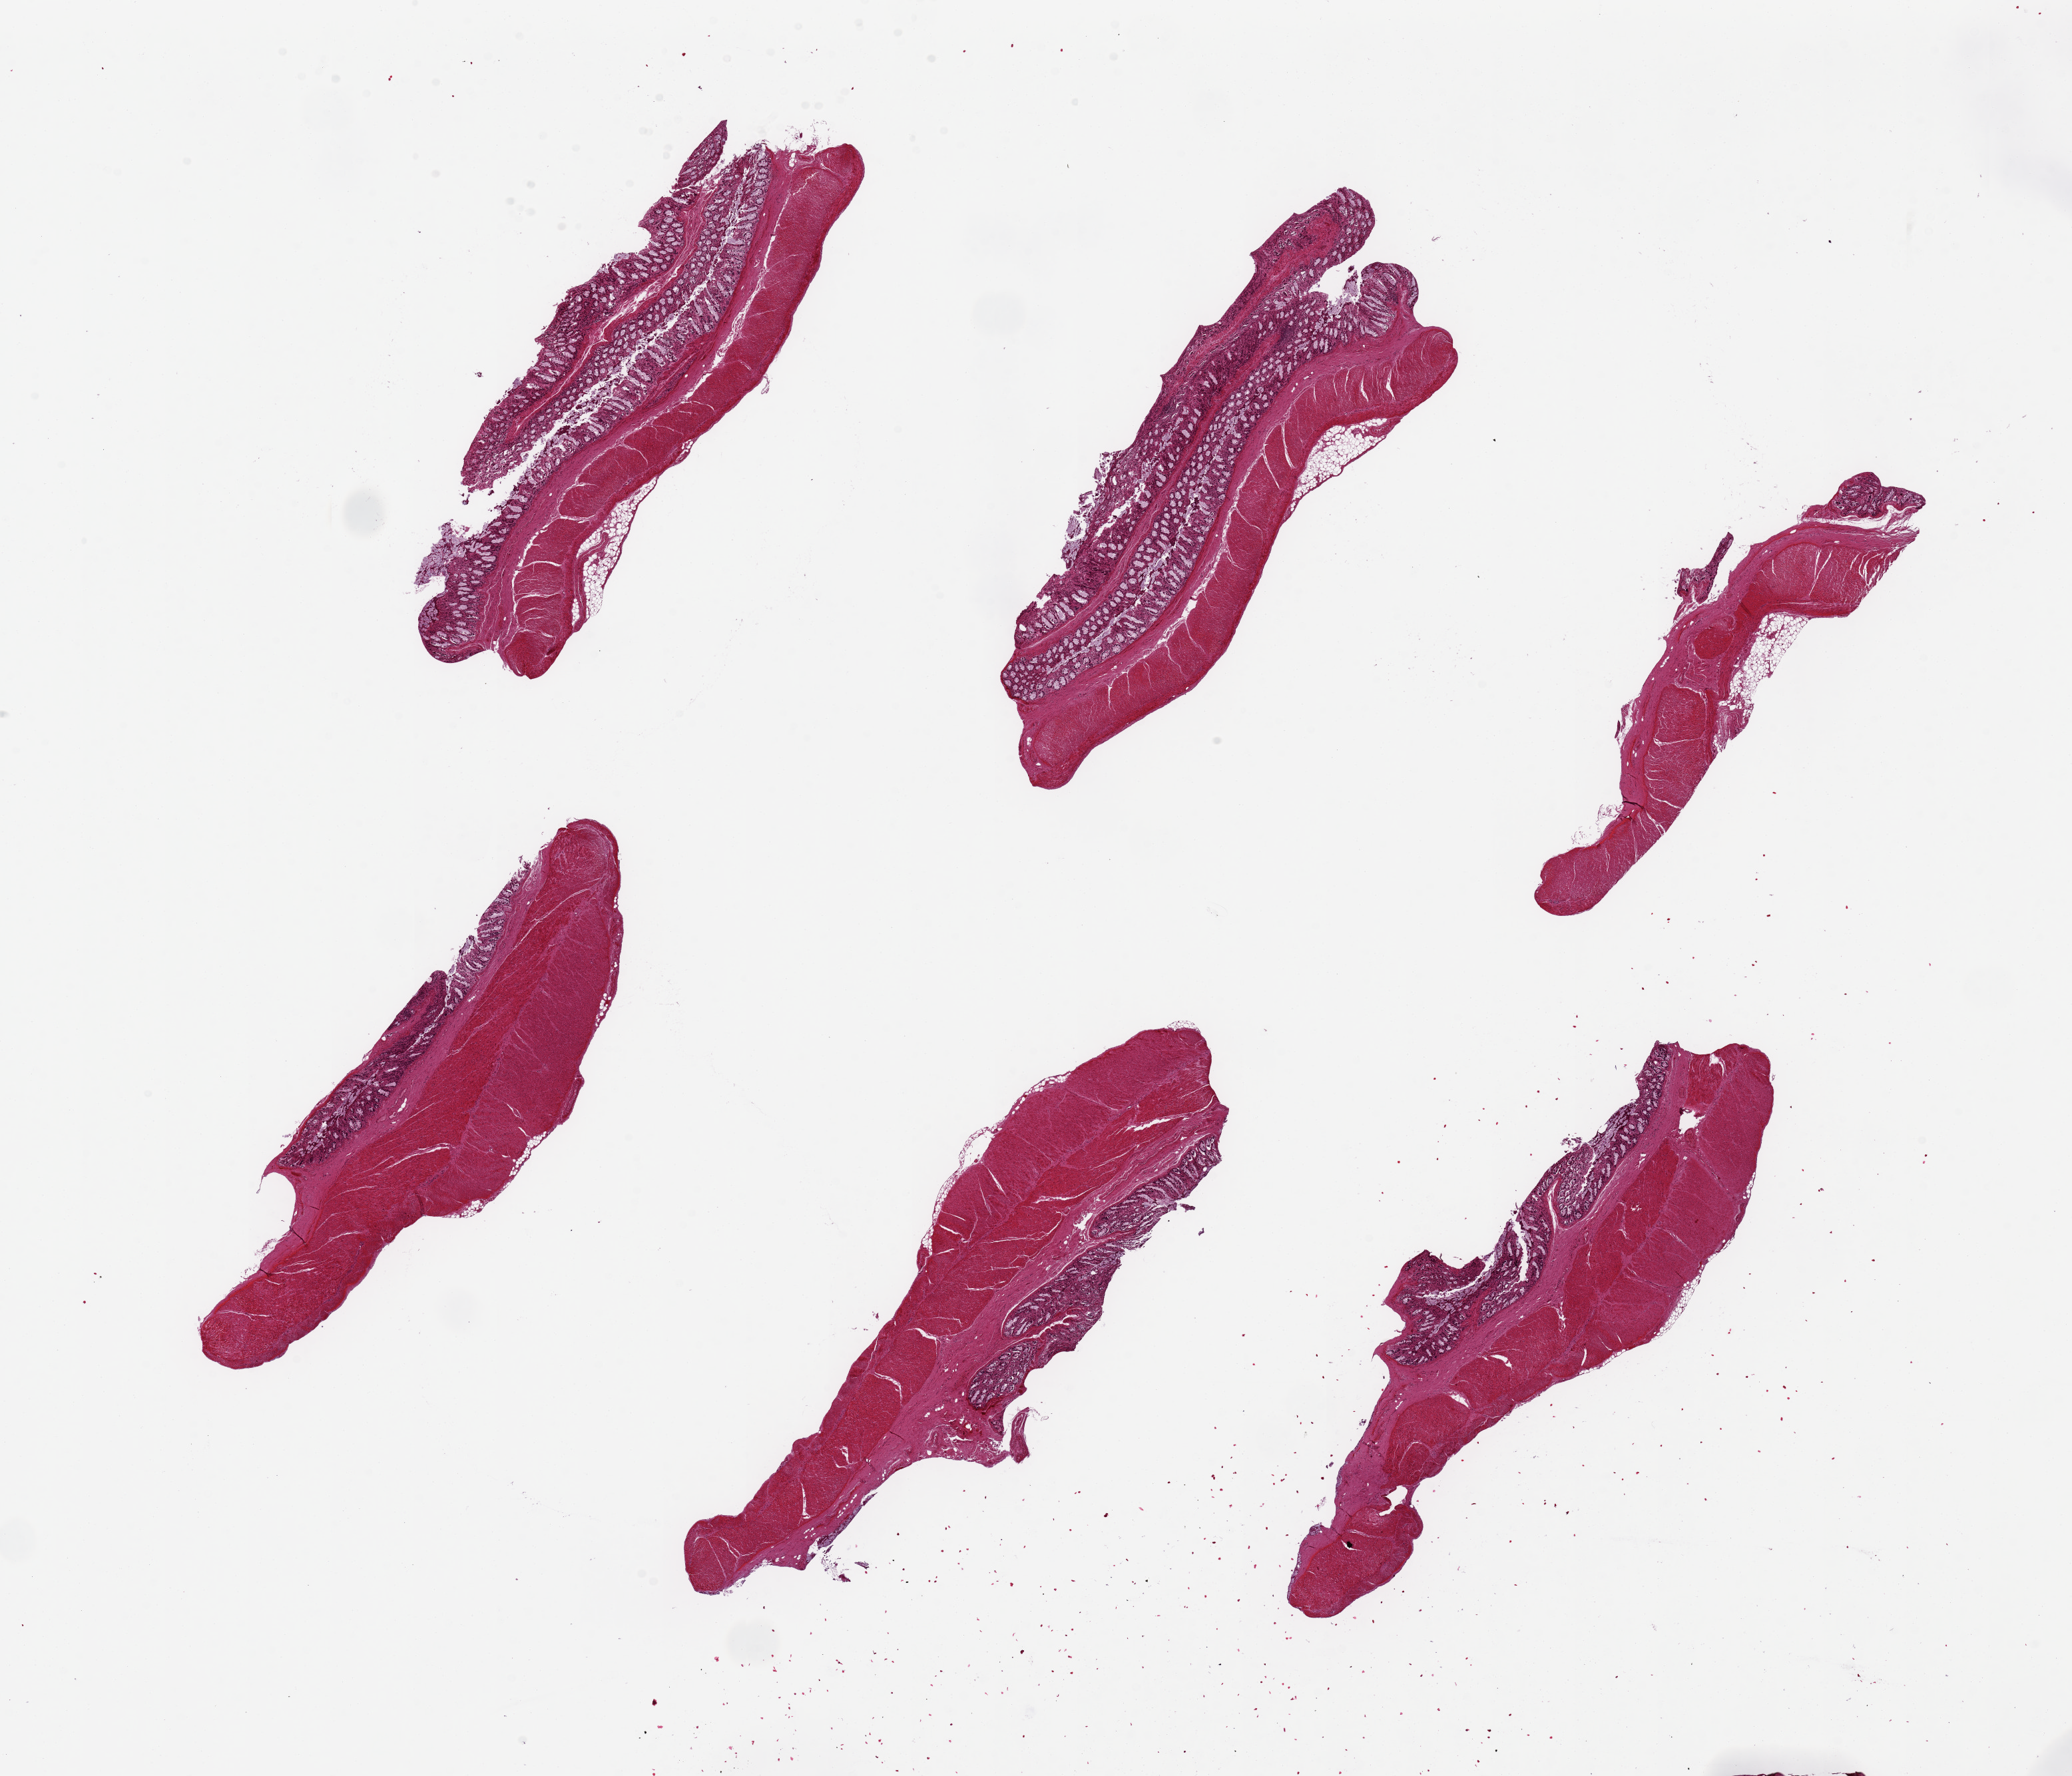
Whole-slide image, haematoxylin and eosin stain — whole scanned area (about 24.6 x 21.1 mm, from a 20x scan) shown as a low-resolution overview. PAXgene-fixed, paraffin-embedded tissue. Sampled site (target tissue): transverse colon. Donor tissue sample. Donor sex: male.
Reviewer comment on this tissue sample: 6 pieces, mucosa badly autolyzed ~7x2mm.